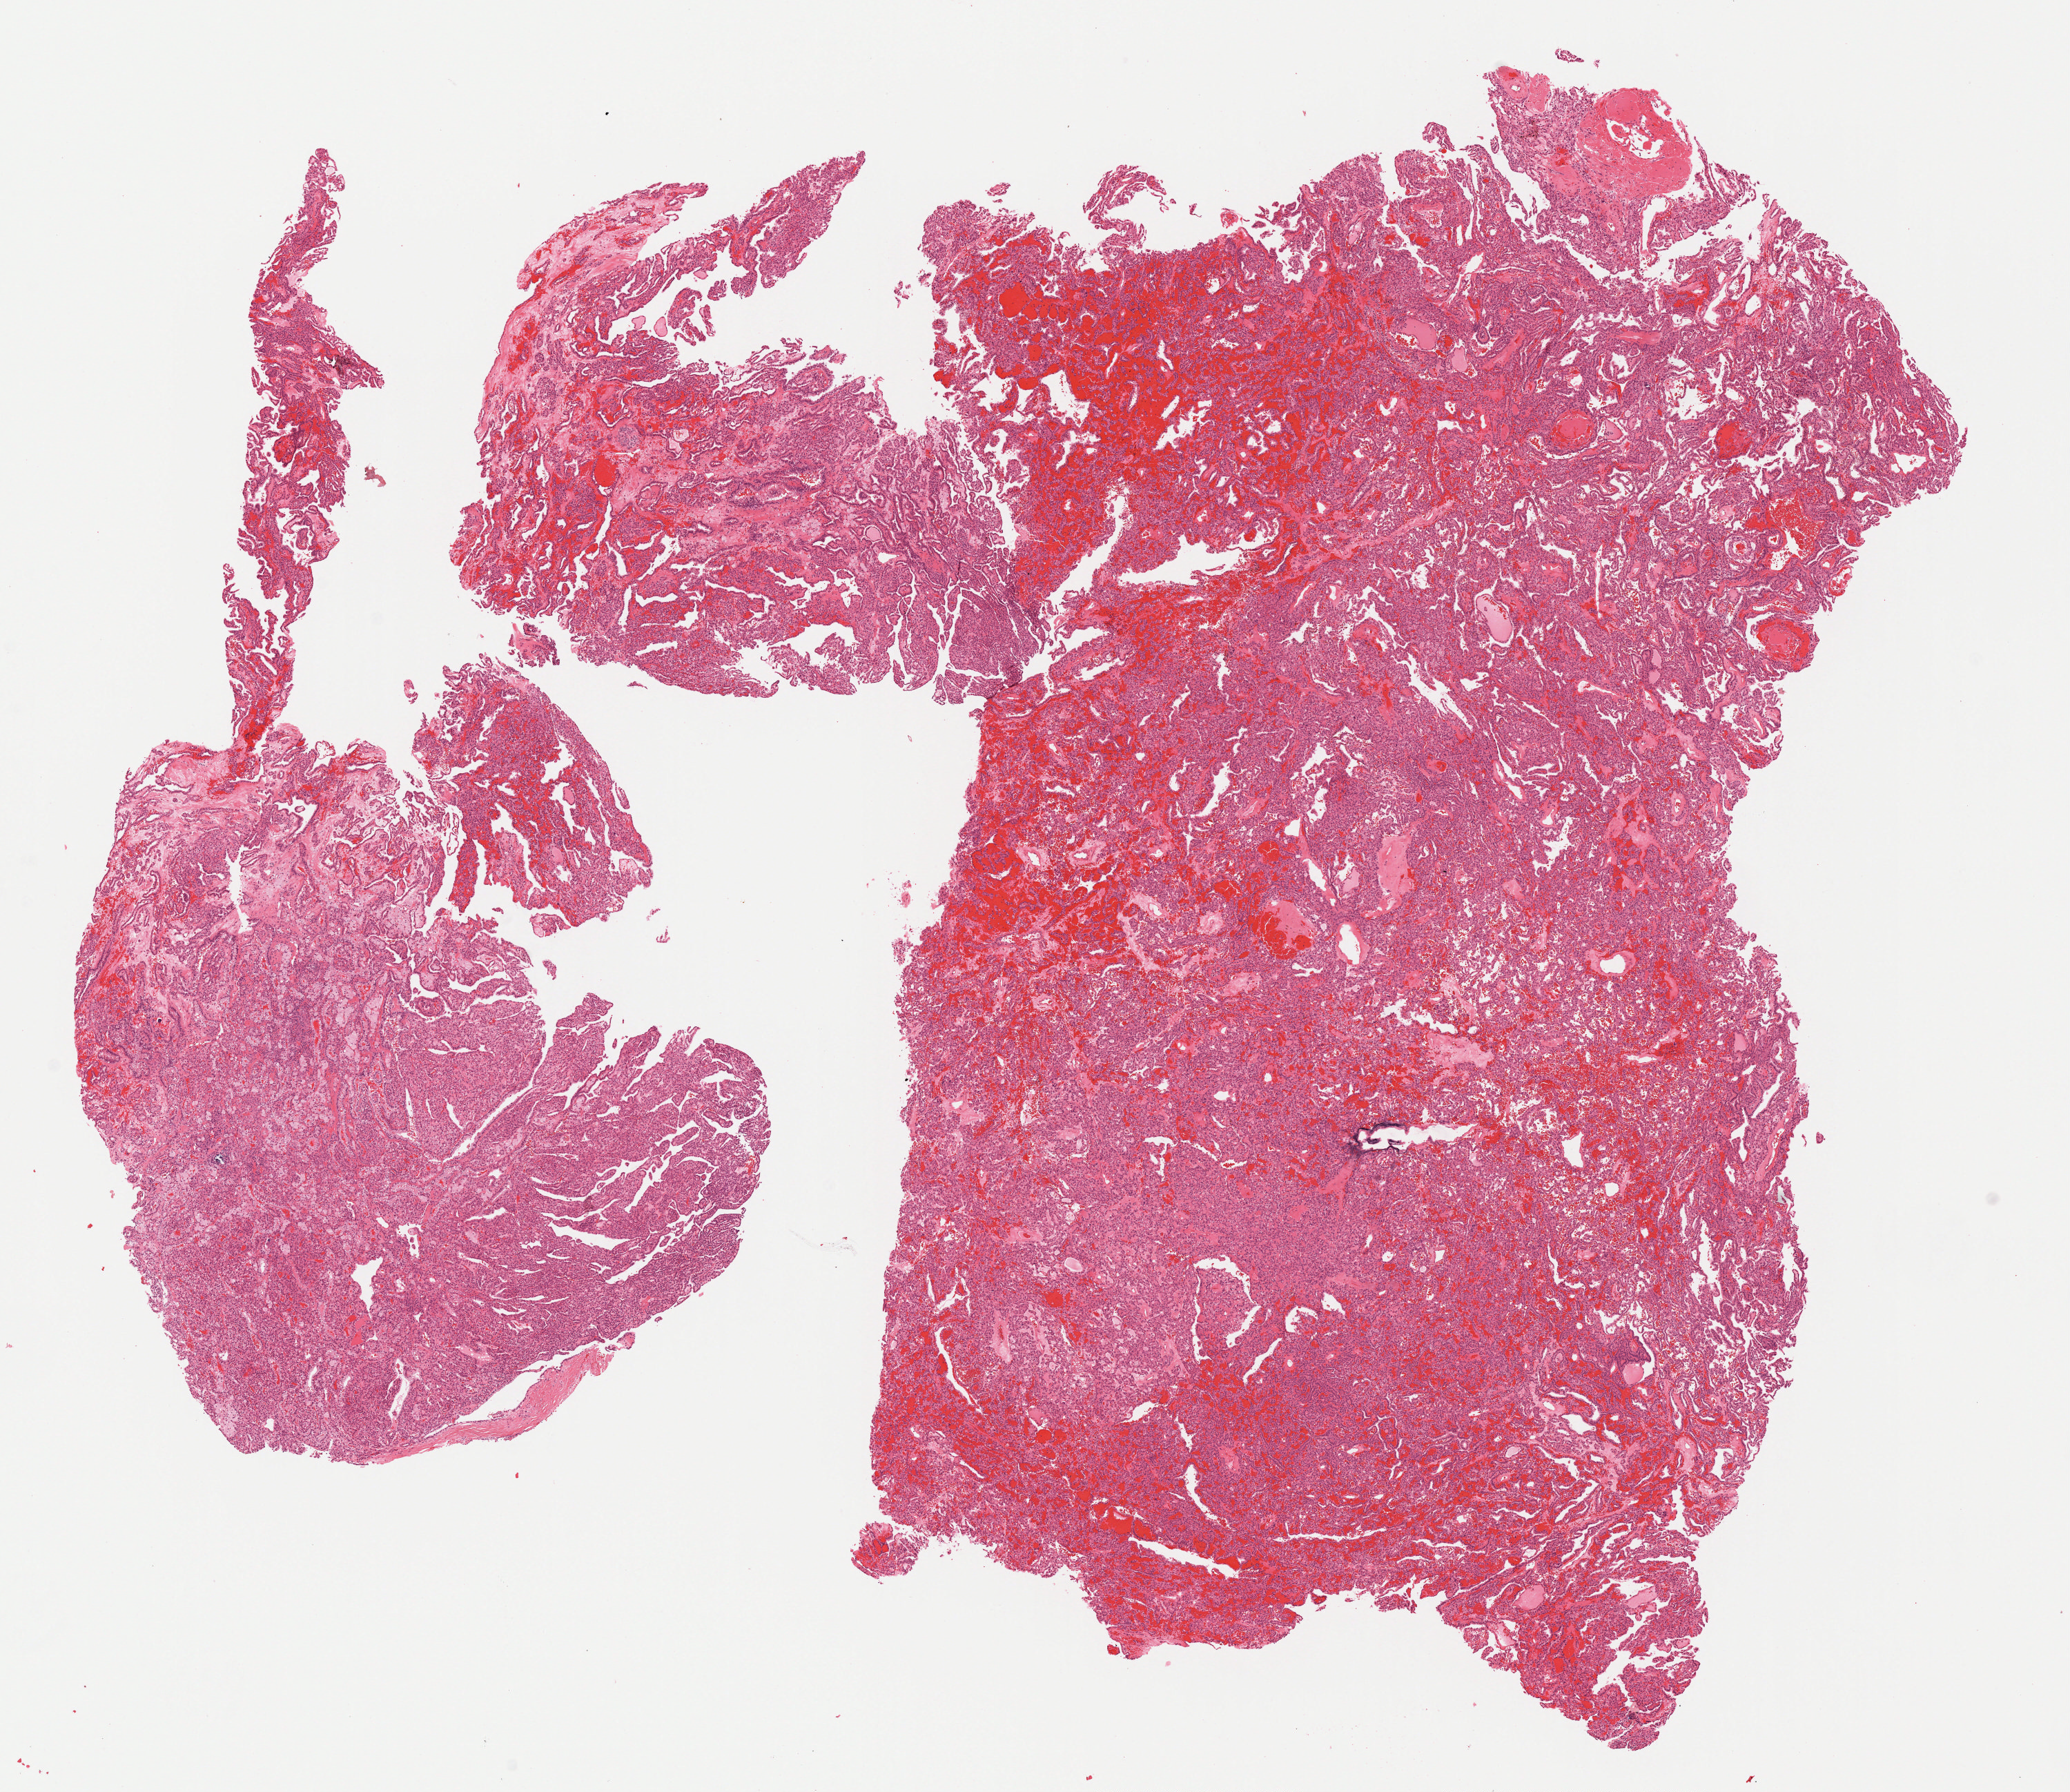
H&E whole-slide image, shown as a low-resolution overview of the whole scanned area (about 12.0 x 10.4 mm, slide scanned at 20x), FFPE section, sample: primary tumour, kidney. Patient: male, age at initial diagnosis 62 years.
• histologic diagnosis: Papillary adenocarcinoma, NOS
• AJCC pathologic stage: I